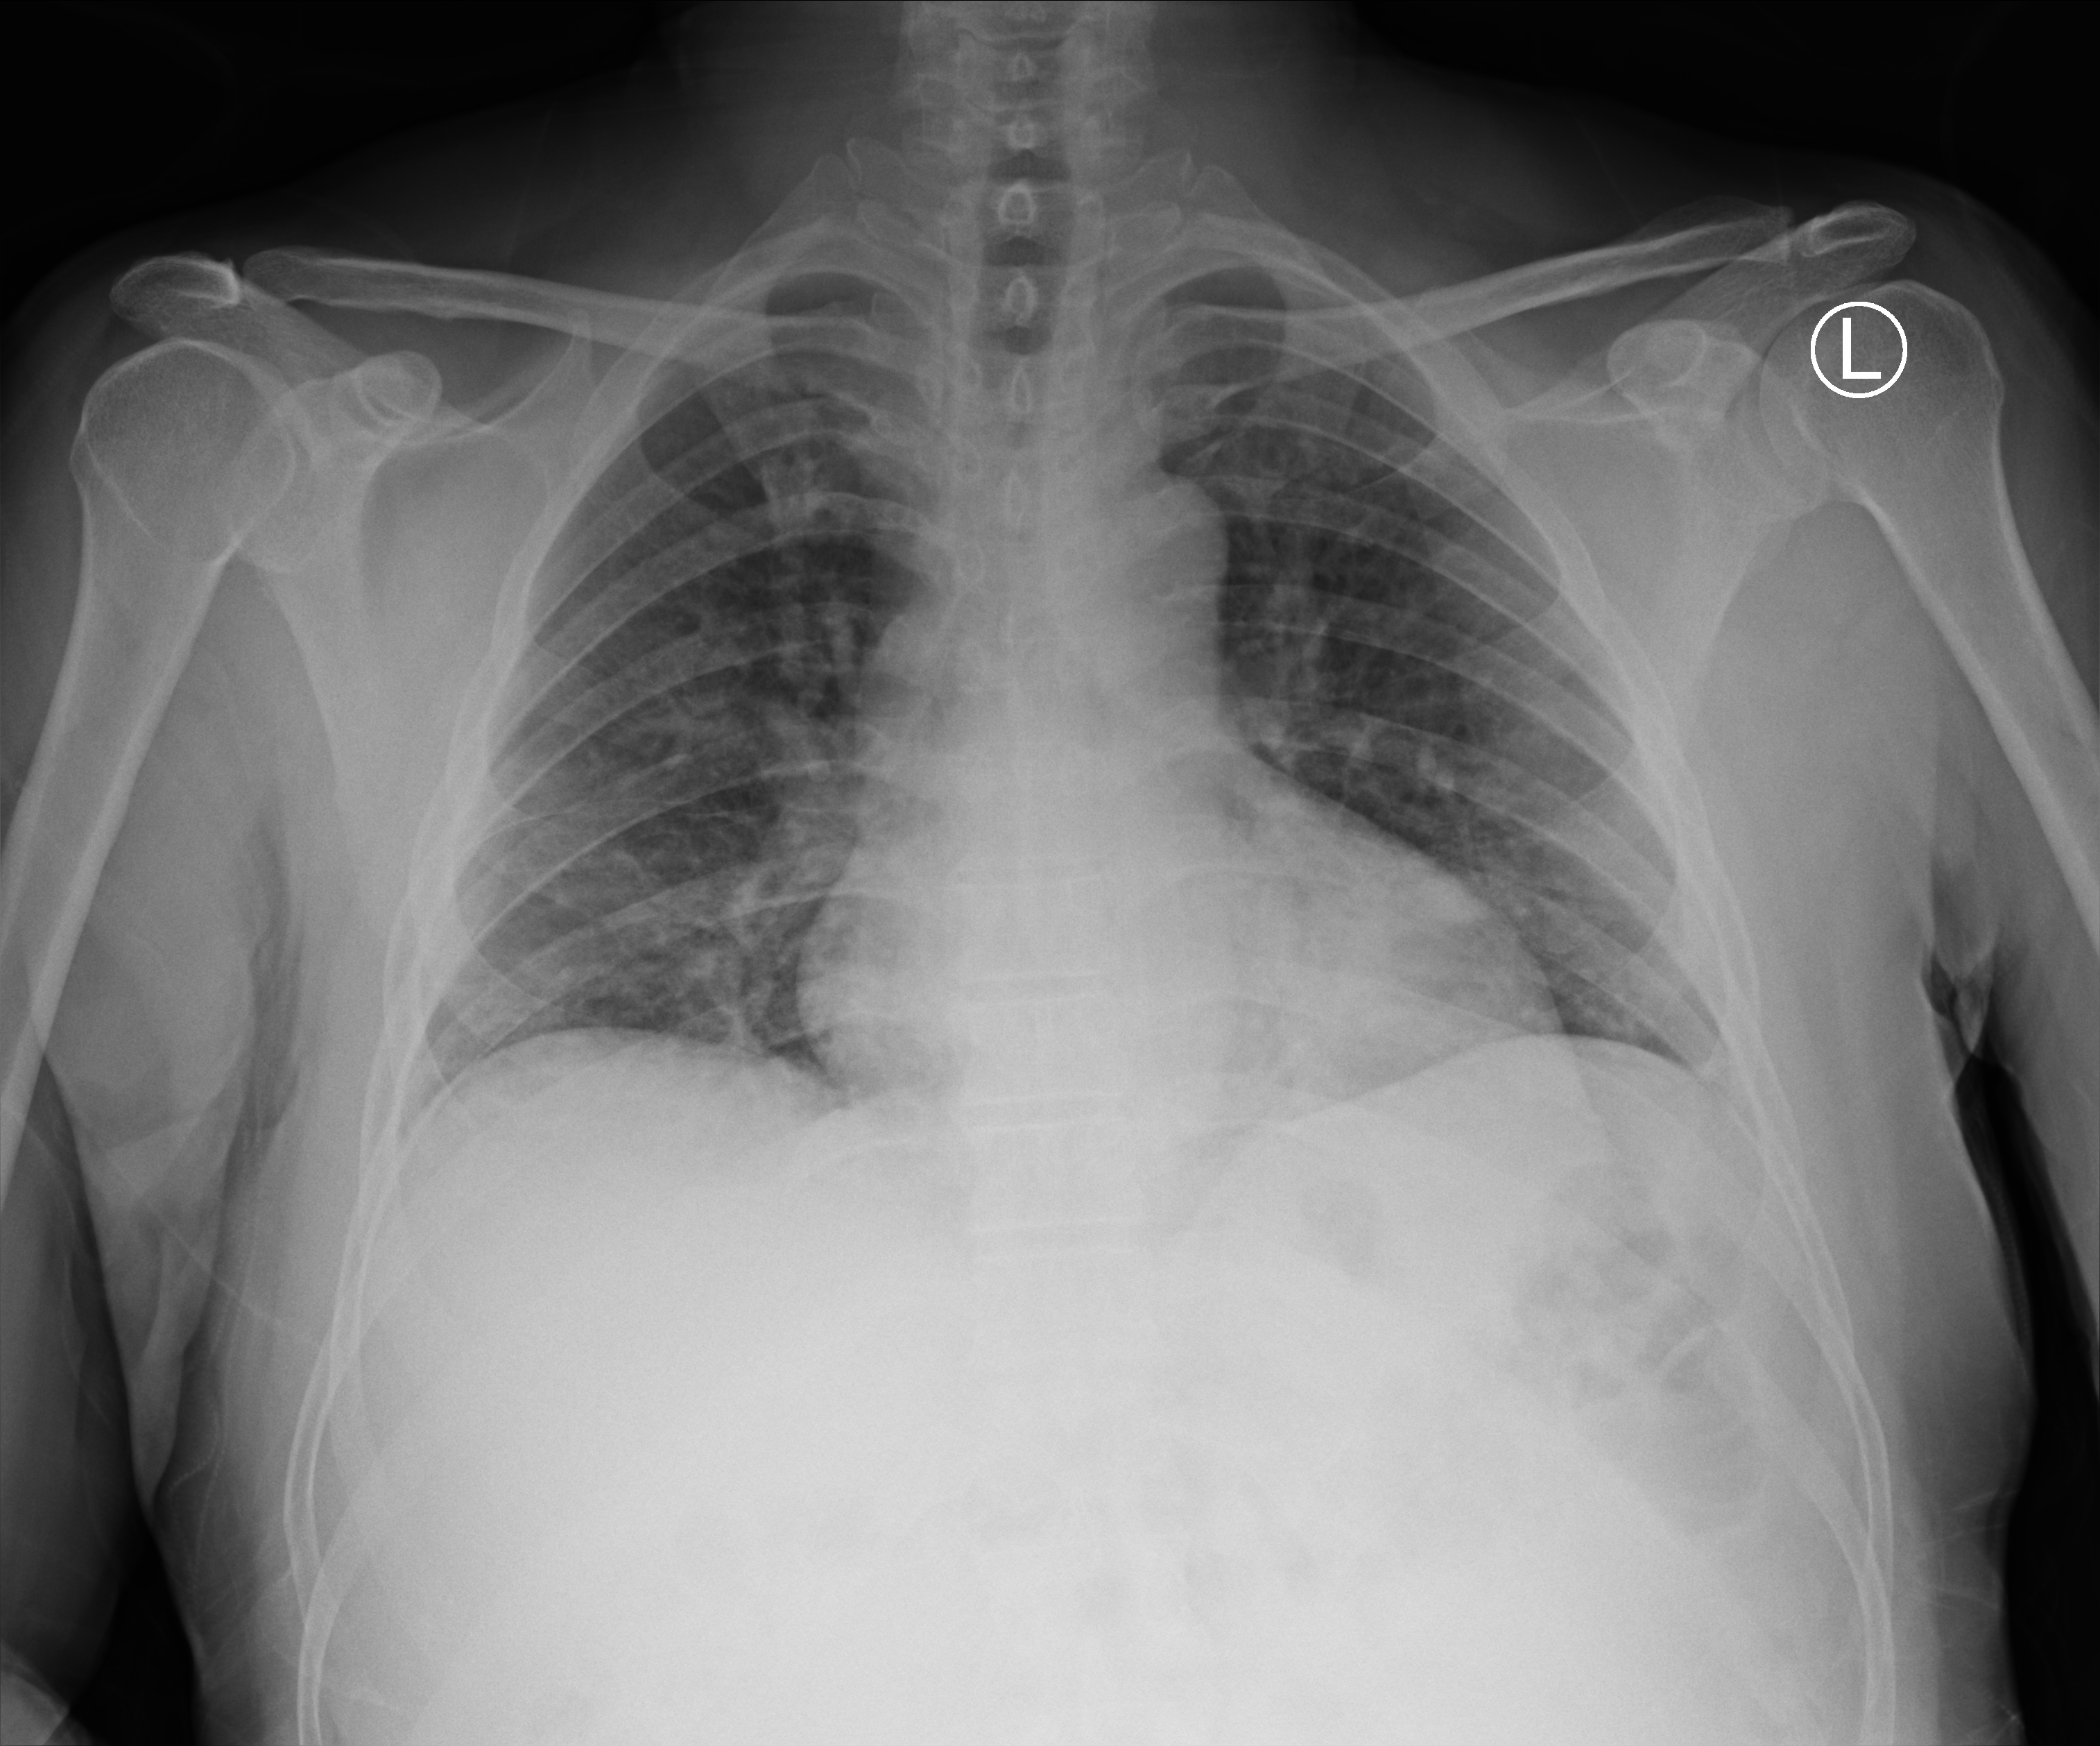
Chest X-ray (portable). Patient hospitalised with COVID-19; male, aged 18–59 years.
Hospital-stay facts (about this admission, not read from this image; timing relative to this image not recorded): length of hospital stay: 2 days; hypertension (admission record): no.